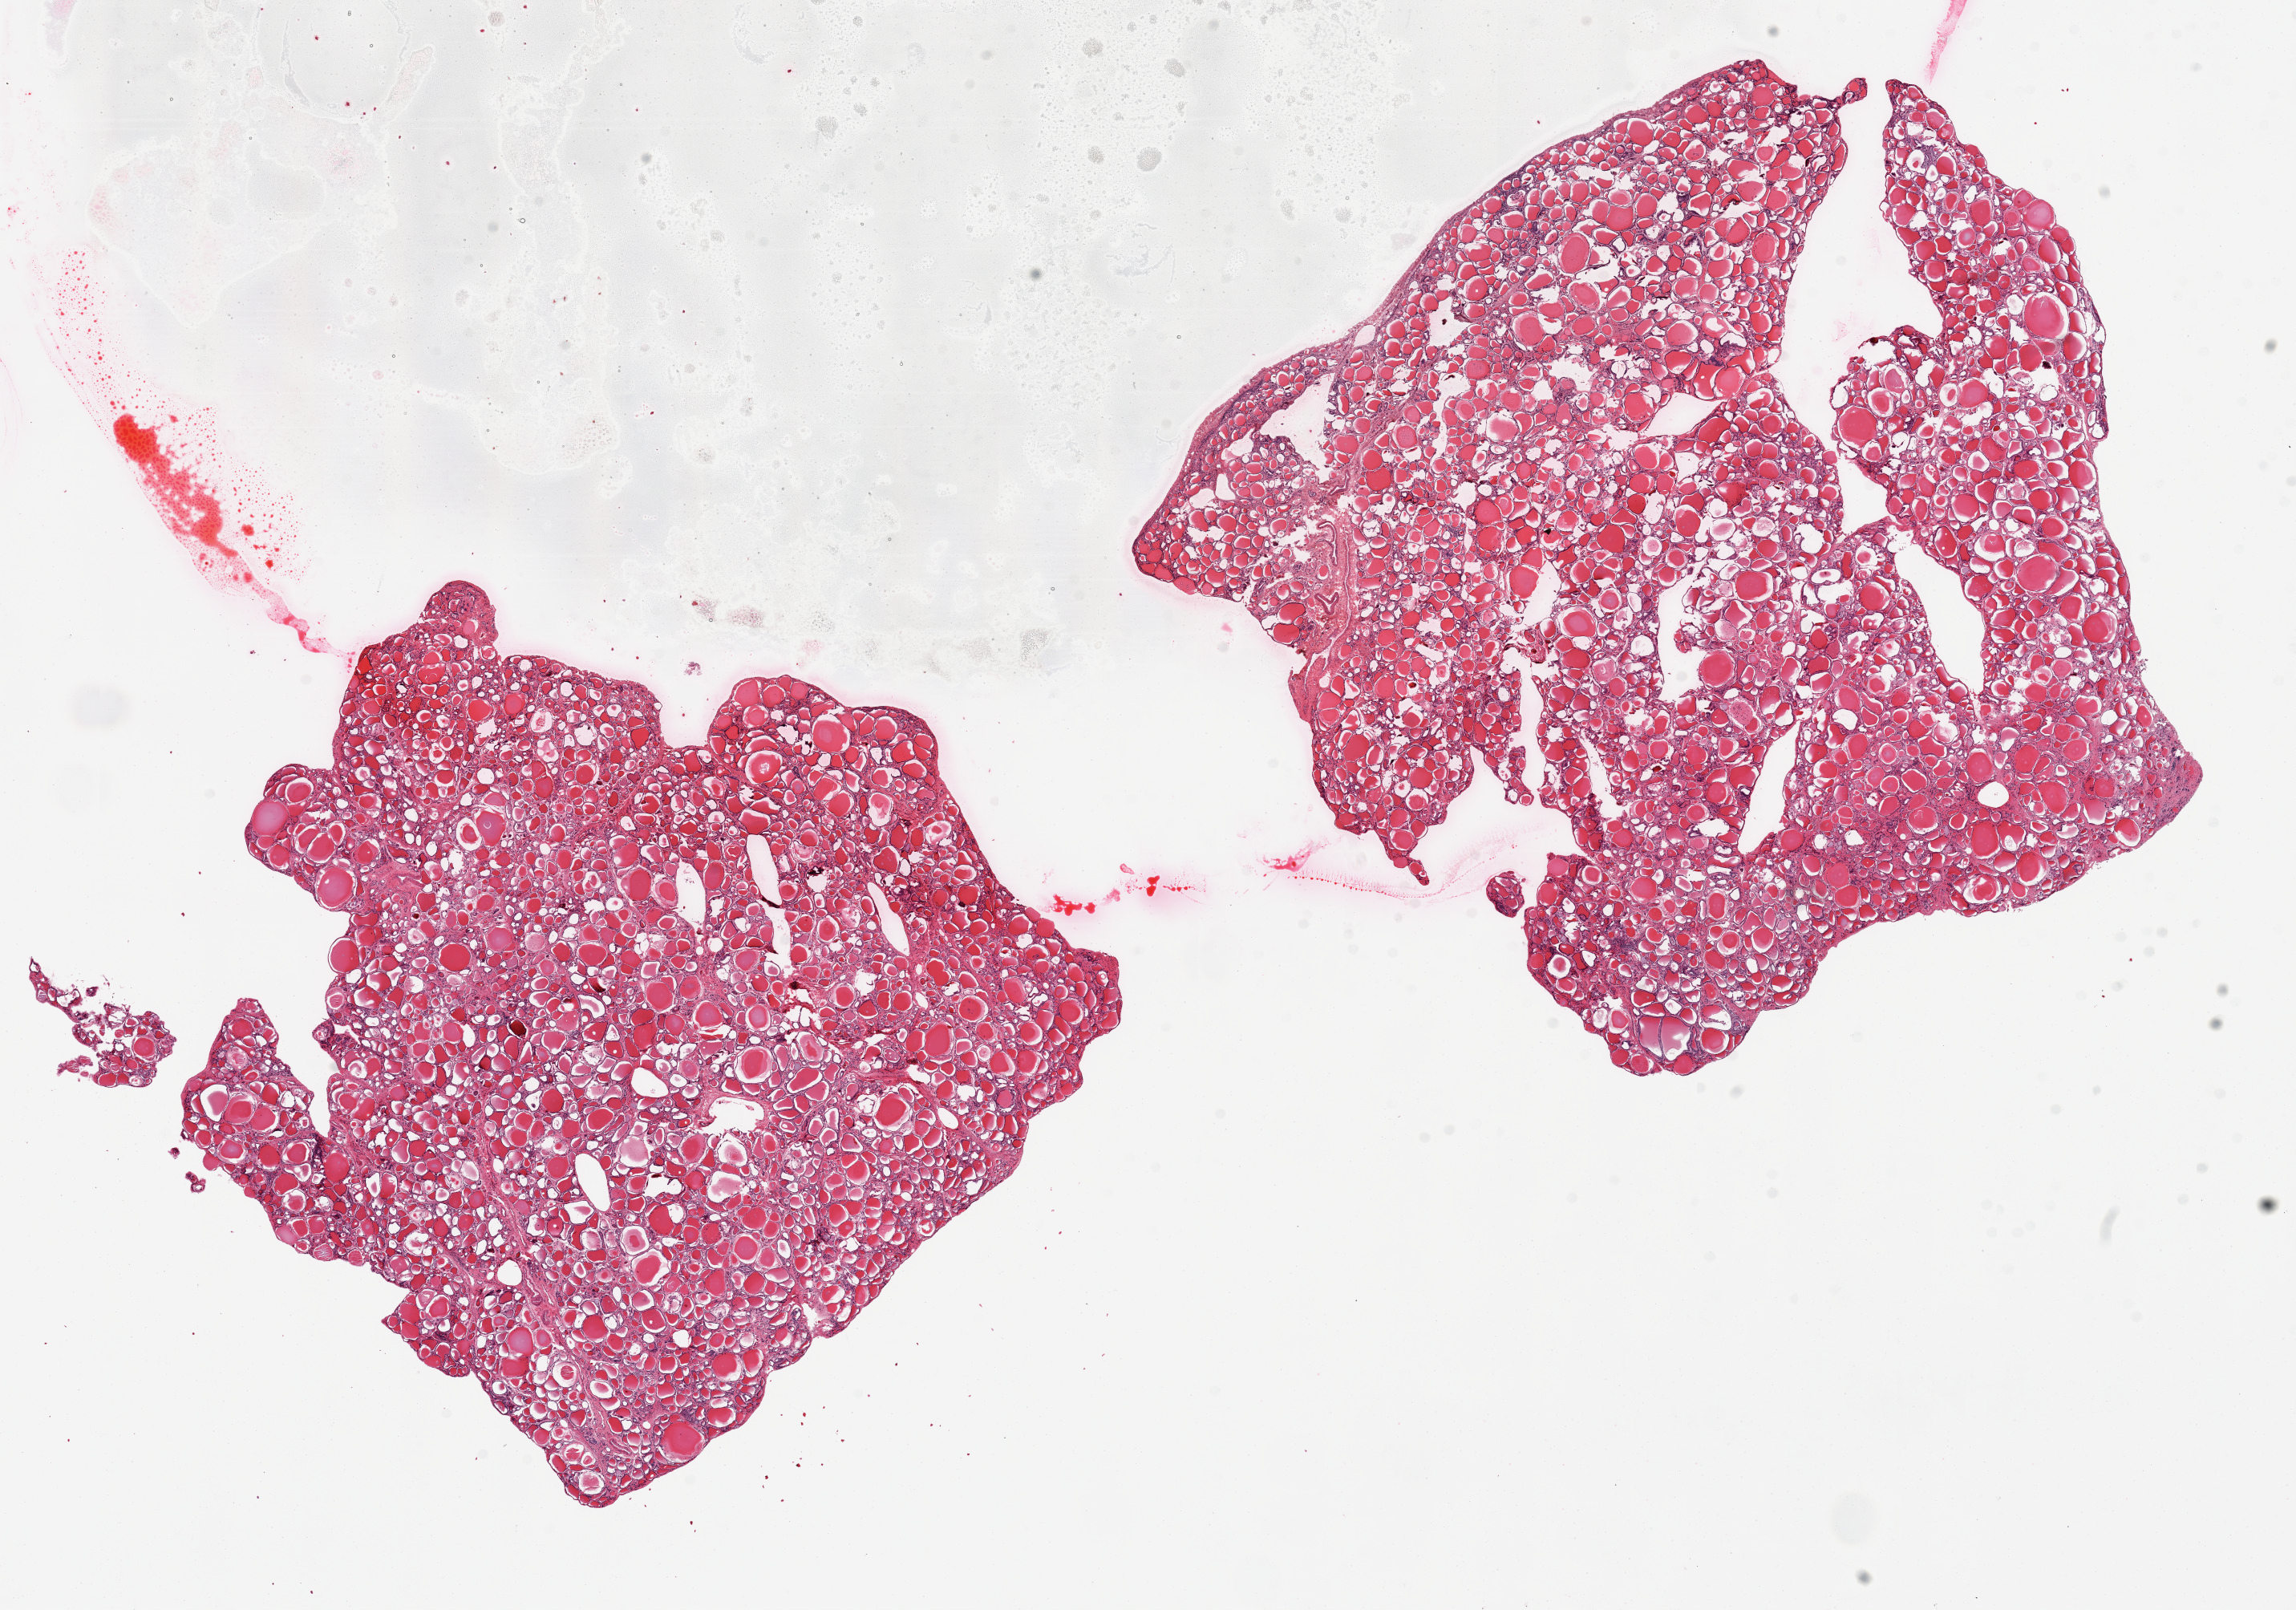
Haematoxylin and eosin whole-slide image, whole scanned area (about 22.6 x 15.9 mm, acquisition: 20x scan) shown as a low-resolution overview; PAXgene-fixed, paraffin-embedded tissue; section of thyroid (target tissue); donor tissue sample. Donor: female.
Review note (as recorded): 2 pieces. 8x8 & 9.5x9mm; Well trimmed.